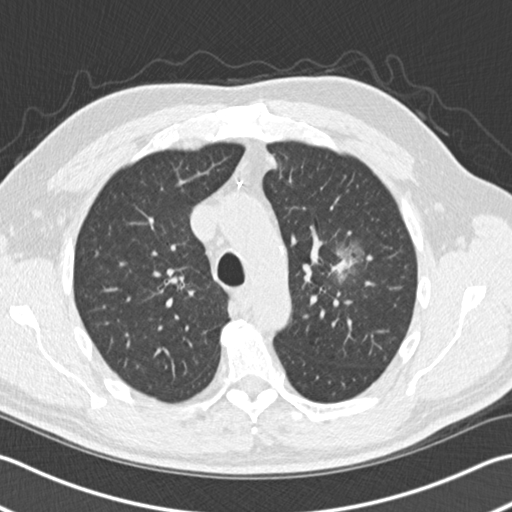
Axial slice from a low-dose chest CT screening exam. Third screening round (two years after baseline). Lung window (W 1500 / L -600 HU). 2 mm slice thickness. Standard (soft-tissue) reconstruction kernel (B30f). 120 kVp. 512 × 512 image matrix. Male, age 65 years at enrolment. Former smoker at enrolment.
• Expert-annotated lung lesion, bounding box <306,241,370,306> (left, top, right, bottom; pixels).
• The screening reader recorded 4 non-calcified nodules or masses ≥4 mm on this exam (left upper lobe, left upper lobe, left lower lobe, right middle lobe); which of them this box marks is not recorded.
• Official screen result: positive, other.
• Participant outcome: lung cancer diagnosed 196 days after this screen — acinar cell carcinoma, left upper lobe, stage IA (AJCC 6th edition), 25 mm at pathology.